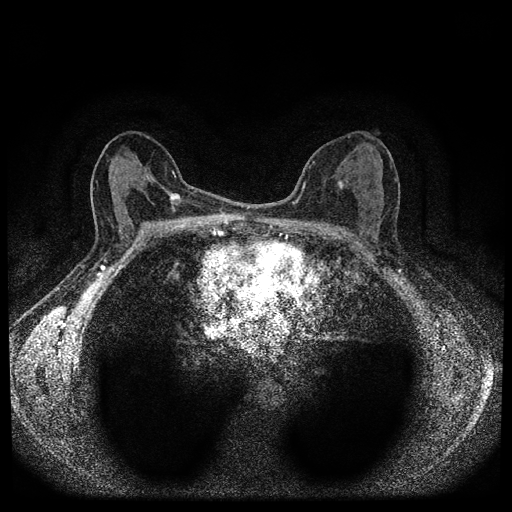
Breast MRI (dynamic contrast-enhanced, multi-phase), one axial slice; position 52 of 112 along the scan axis; dynamic contrast-enhanced series, time point 2 of 5 at this slice position (early post-contrast); 1.5 T; TE 2.7 ms, TR 5.4 ms; 2 mm slice thickness; 512 × 512 image matrix, field of view 320 × 320 mm. Patient: female, 61 years.
Outlined on this slice (semi-automatically segmented with operator editing):
- breast lesion (labelled benign in the annotation): box from (x=336, y=179) to (x=348, y=190) px
- breast lesion (labelled 'tumour' in the annotation; benign lesions carry a separate 'benign' label): (x=169, y=192)–(x=181, y=206)